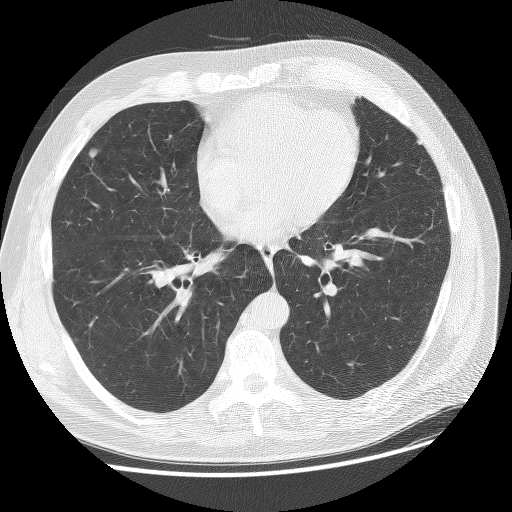
Low-dose screening chest CT, one axial slice. Position 65 of 137 along the scan axis. Reconstruction kernel BONE. Lung window (W 1500 / L -600 HU). 2.5 mm slice thickness. 512 × 512 image matrix, field of view 380 × 380 mm.
Annotated regions visible in this slice (expert manual segmentation):
- lesion 3 (tumor, upper lobe of right lung): bounding box [x1, y1, x2, y2] px = [90, 150, 97, 157]